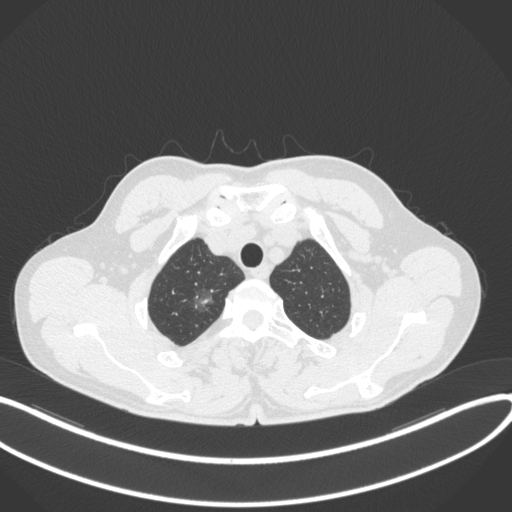
Chest CT, one axial slice. Slice 335 of 407 in the series (ordered by position). 120 kVp. Lung window (W 1500 / L -600 HU). 1 mm slice thickness. 512 × 512 image matrix, field of view 400 × 400 mm. Patient: male, 58 years. Case-level facts recorded for this patient, not image findings: clinical TNM (as recorded): T1c N0 M0; histopathological grade: G1-2.
Outlined on this slice (rectangle marked by the reading radiologist):
- lung tumour (recorded histology: adenocarcinoma): bounding box <189,286,217,314> (left, top, right, bottom; pixels)